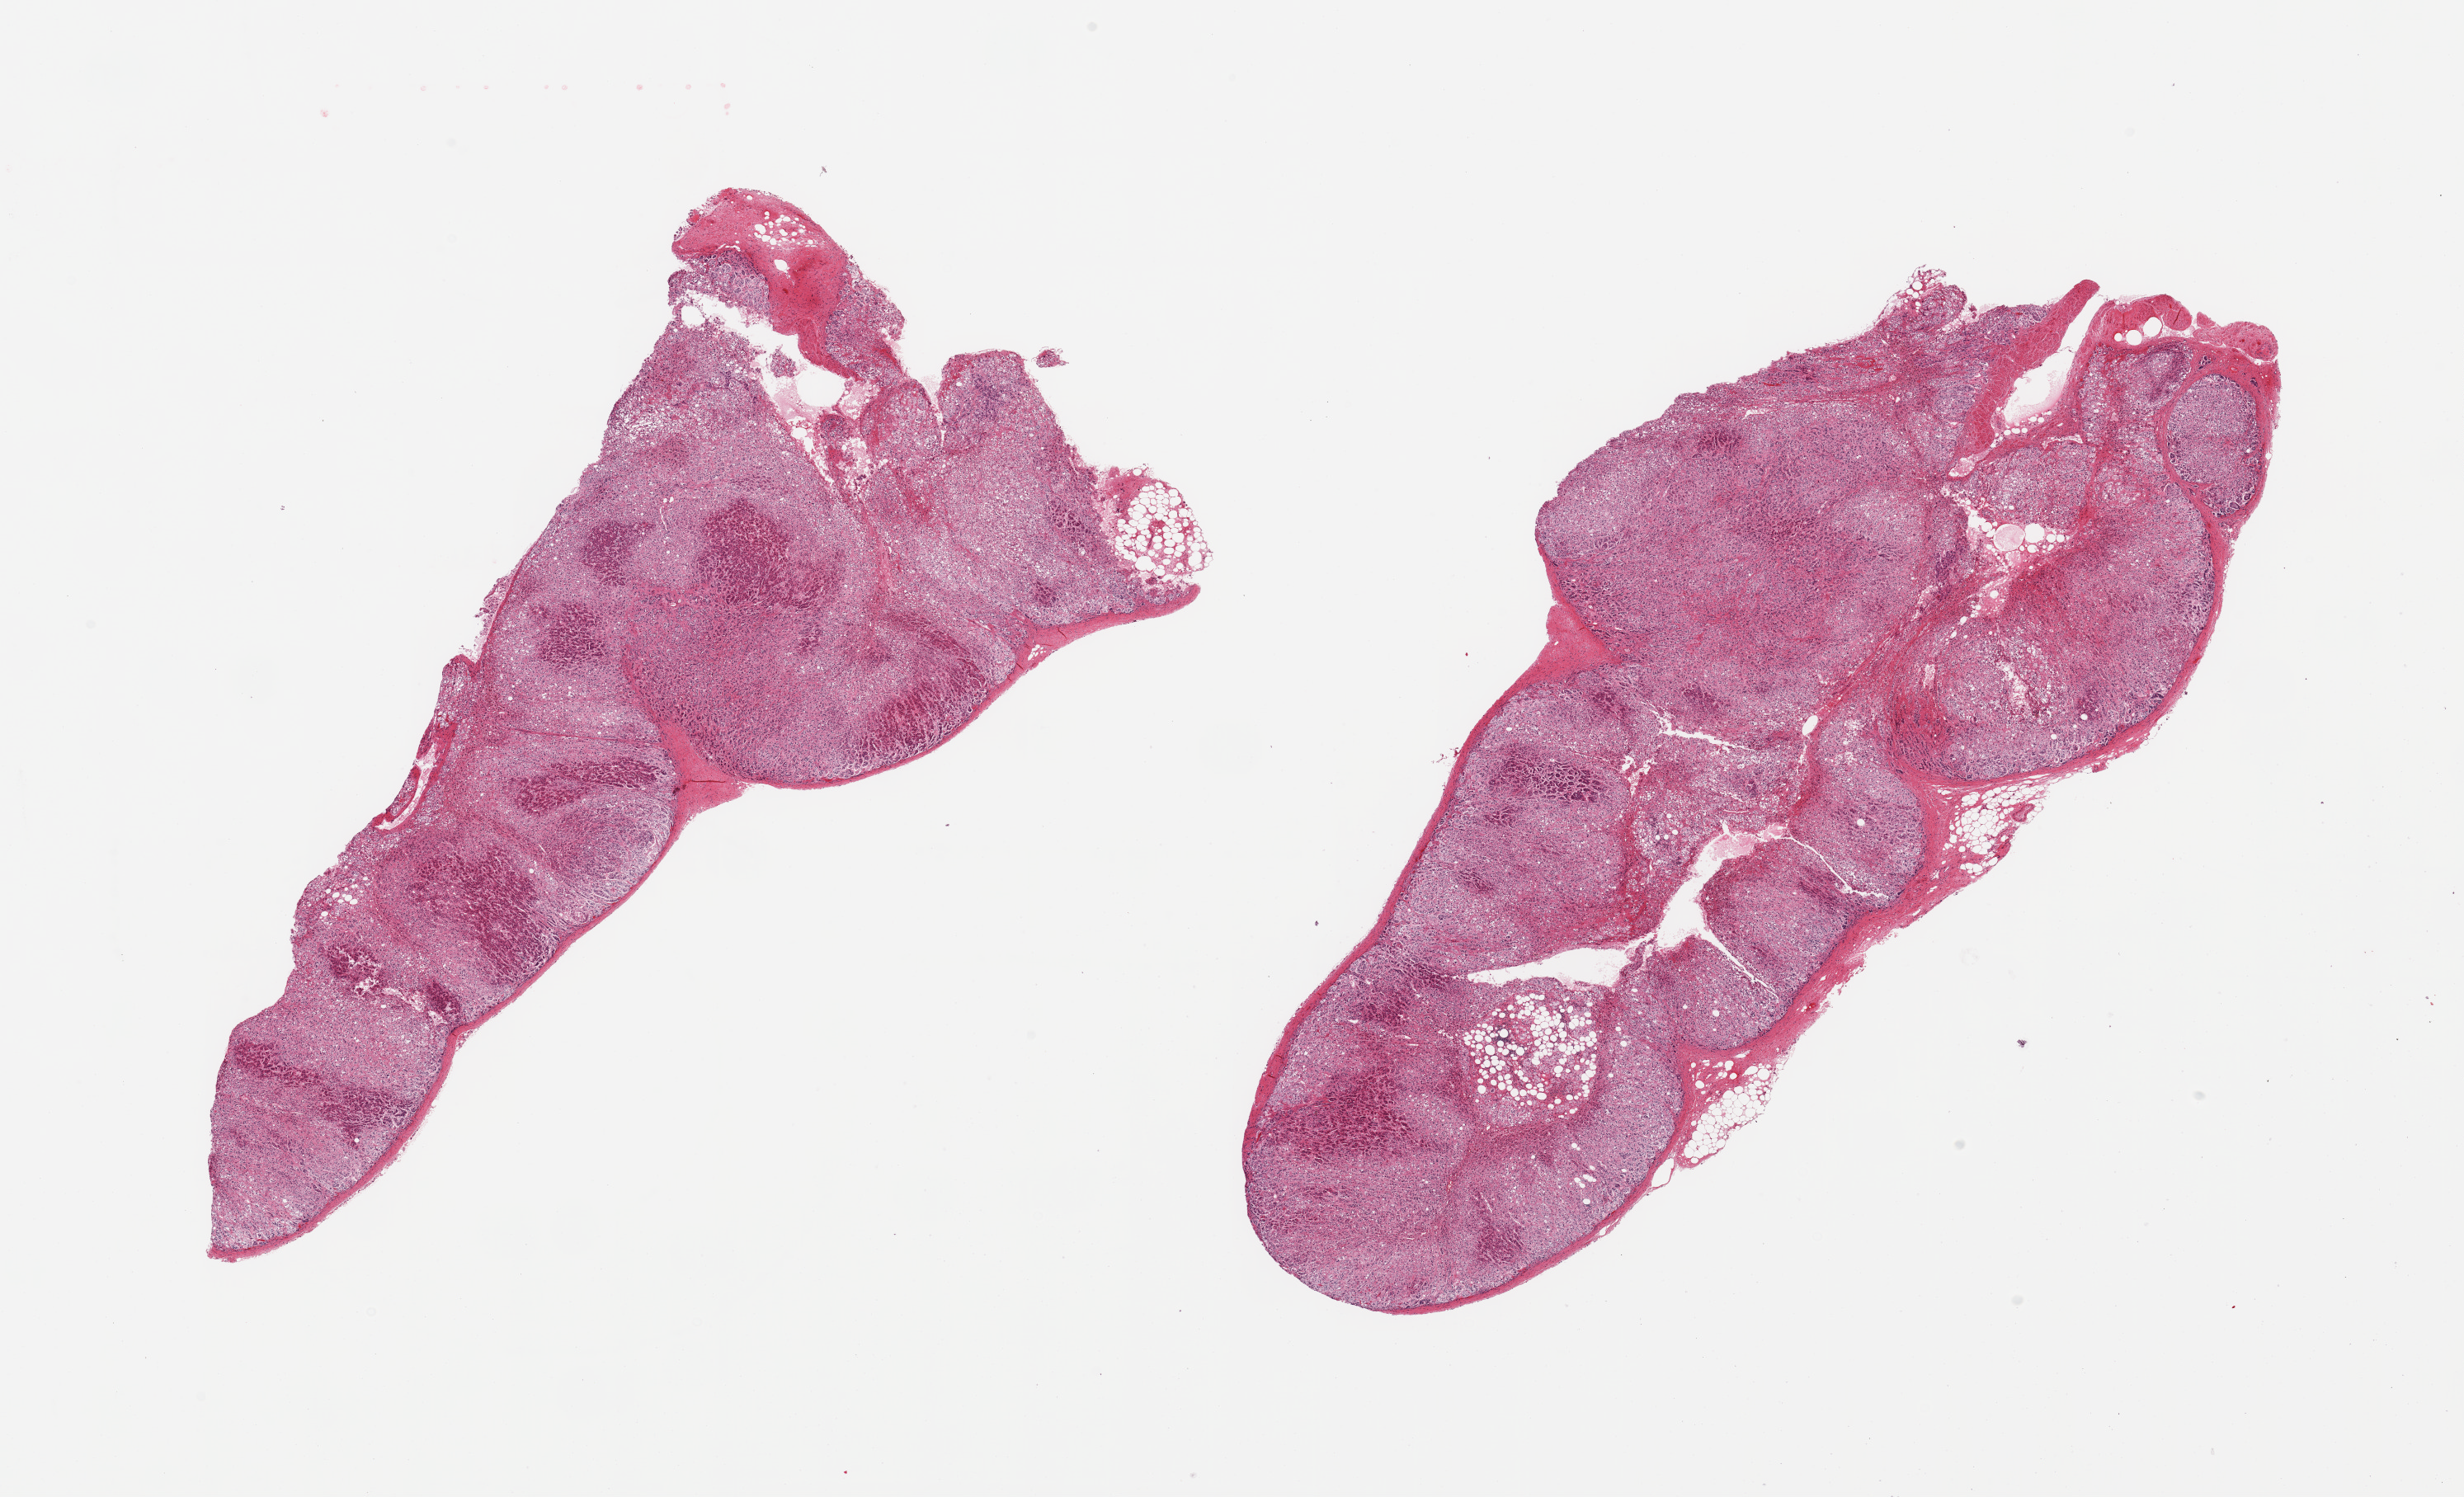
Digitized hematoxylin and eosin (H&E)-stained section, whole scanned area (about 23.6 x 14.4 mm, slide scanned at 20x) shown as a low-resolution overview, PAXgene-fixed paraffin-embedded (PFPE) section, target tissue: adrenal gland, donor tissue sample. Male donor.
Reviewer comment on this tissue sample: 2 pieces, moderately autolyzed cortex.